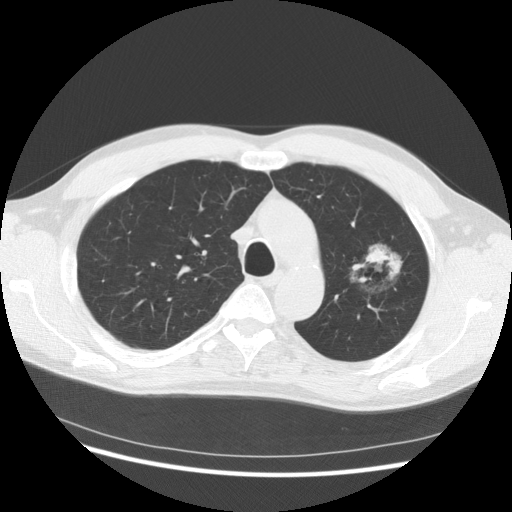
Low-dose screening chest CT, one axial slice. Slice 104 of 145 in the series (ordered by position). Reconstruction kernel STANDARD. Lung window (W 1500 / L -600 HU). 2.5 mm slice thickness. 512 × 512 image matrix, field of view 370 × 370 mm.
Annotated regions visible in this slice (outlined manually by an expert reader):
- lesion 1 (tumor, upper lobe of left lung): bounding box (x1, y1, x2, y2) in pixels: (366, 245, 401, 272)